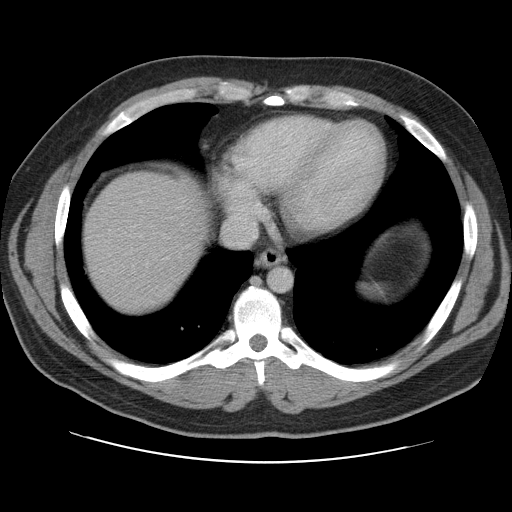
Contrast-enhanced abdominal CT, one axial slice; position 100 of 109 along the scan axis; 120 kVp; intravenous contrast given; soft-tissue window (W 400 / L 40 HU); 5 mm slice thickness; 512 × 512 image matrix, field of view 402 × 402 mm. Male patient, age 35 years. From the clinical record (not read from this slice): diagnosis: colorectal cancer liver metastases, imaged before liver resection; multiple liver metastases: yes; largest metastasis: 2.8 cm; disease in both lobes: yes.
Annotated regions visible in this slice (manually delineated by an expert):
- liver: box from (x=82, y=172) to (x=206, y=314) px
- planned liver remnant (the part of the liver to remain after resection): (x=82, y=172)–(x=206, y=313)